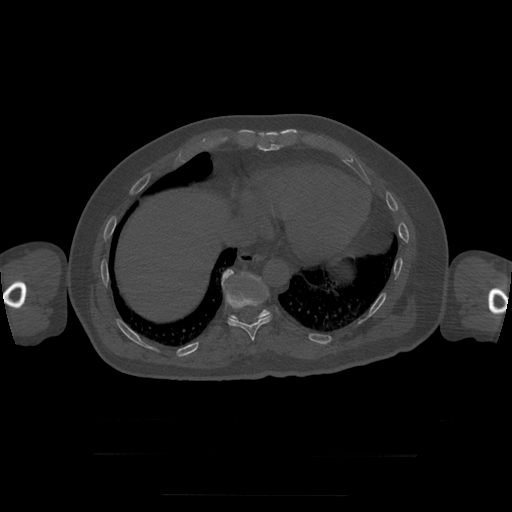
CT including the spine, one axial slice; slice 117 of 397 in the series (ordered by position); reconstruction kernel STANDARD; bone window (W 1800 / L 400 HU); 512 × 512 image matrix. Patient age 73 years. Case-level facts recorded for this patient, not image findings: primary cancer: prostate.
Structures marked on this image (semi-automatic segmentation, software-assisted and operator-edited):
- T10 vertebra: bounding box <222,269,273,341> (left, top, right, bottom; pixels)
- T11 vertebra: <231,273,271,323>